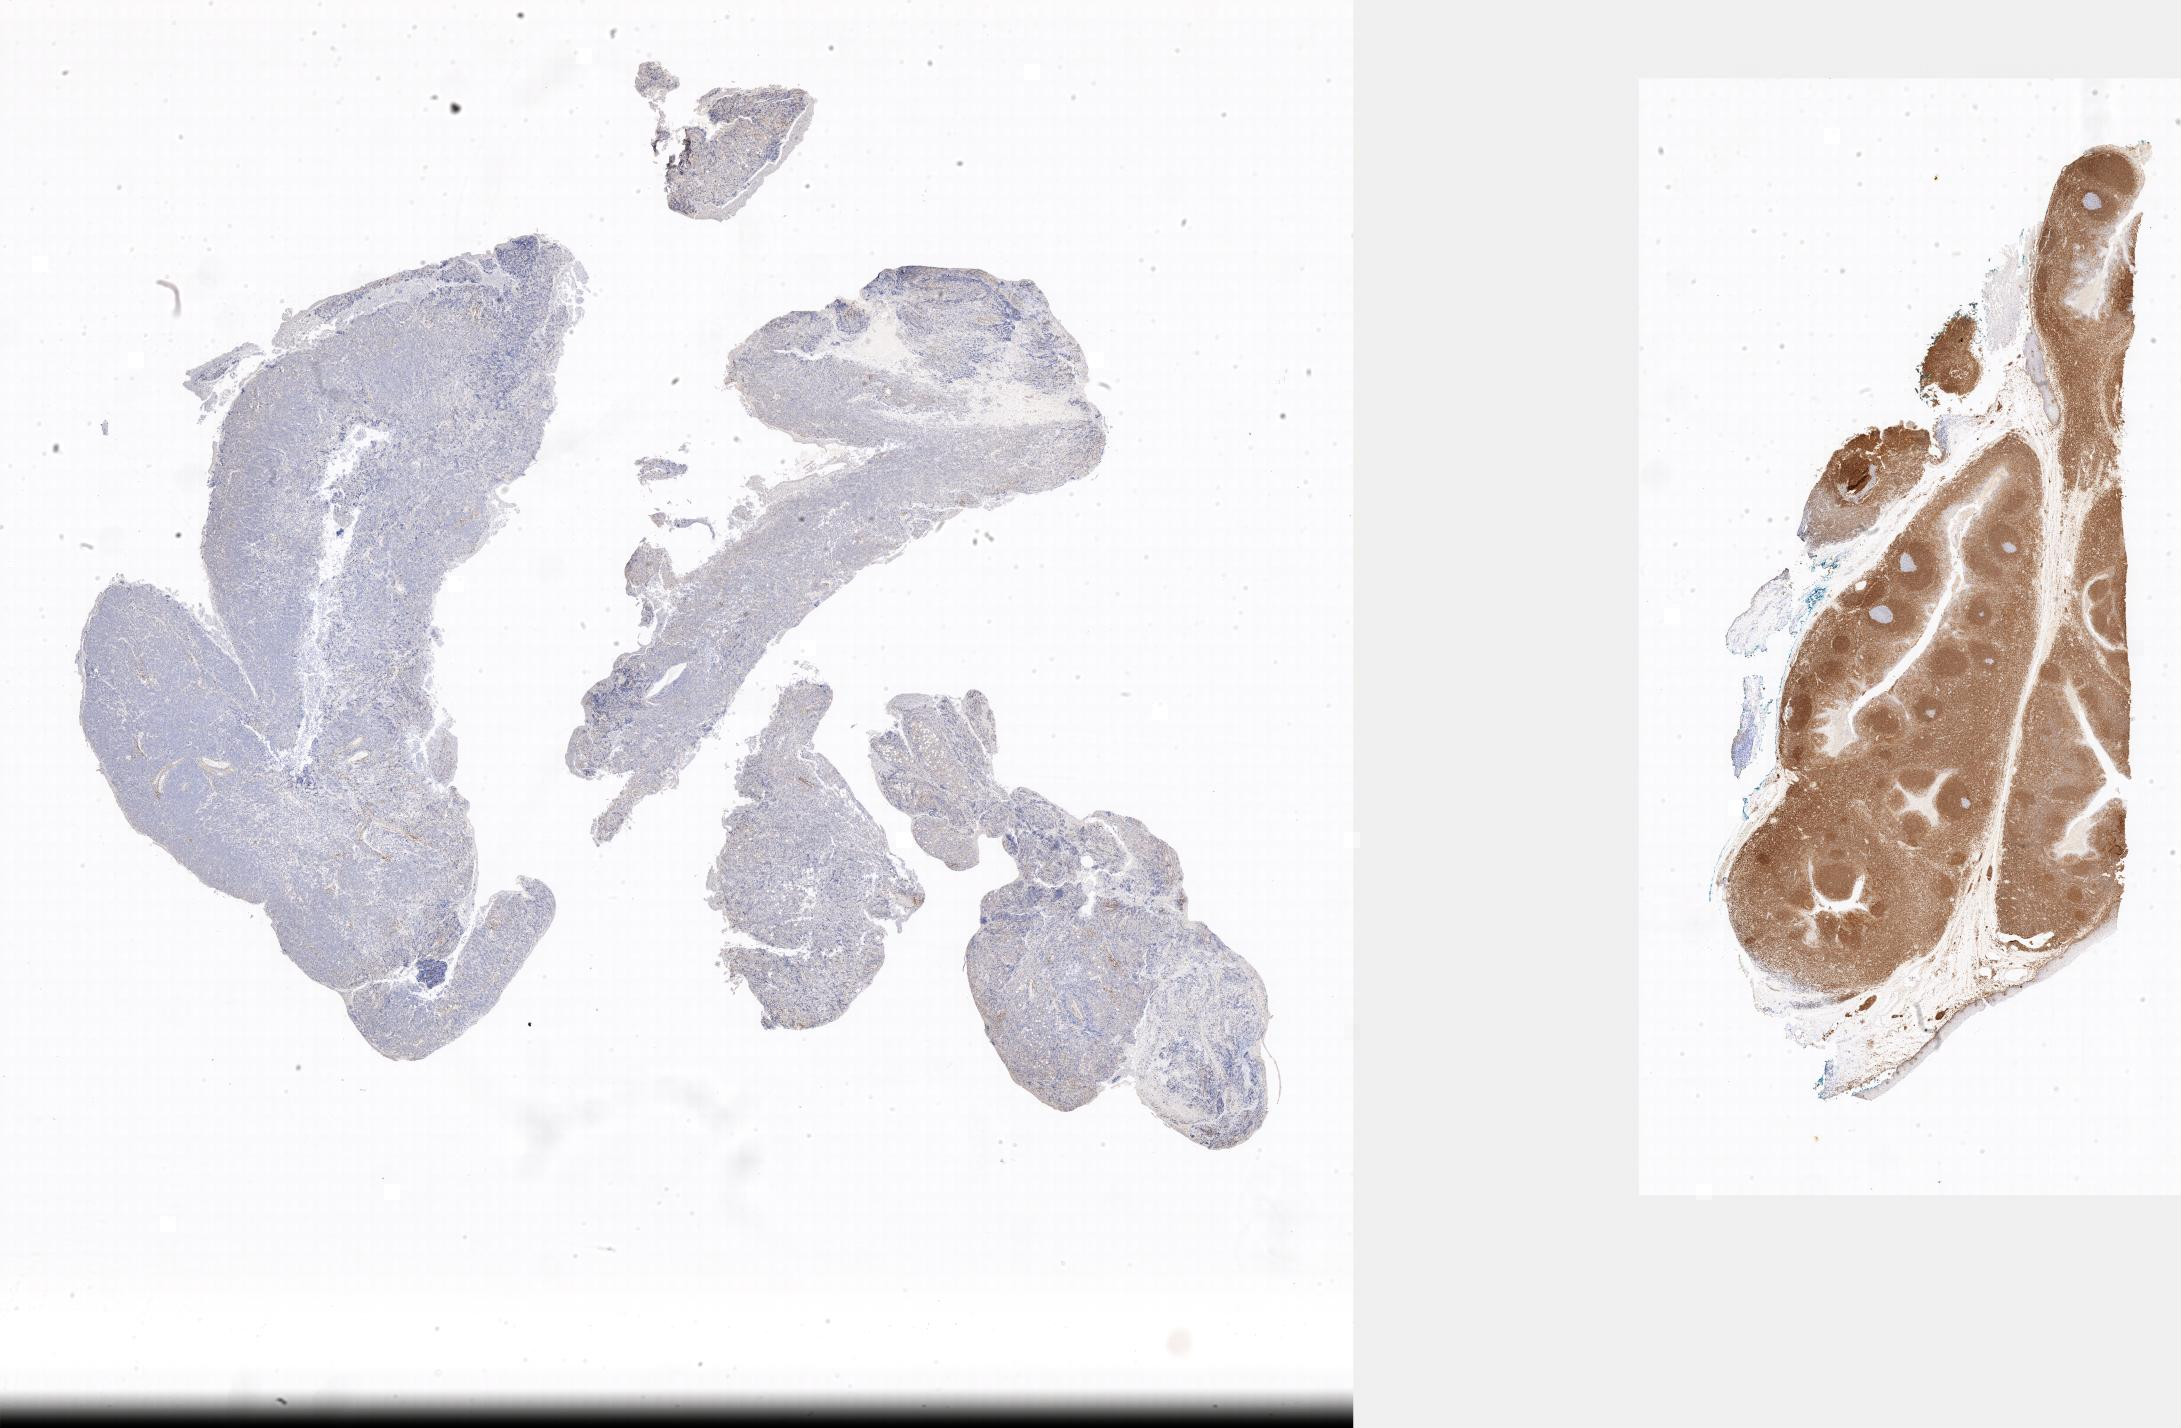
Immunohistochemistry (IHC) whole-slide image stained for BCL2 — low-resolution overview of the scanned area, tumor tissue, anatomic site: abdomen proper. Patient: male, age at initial diagnosis 5 years.
Histologic diagnosis: Burkitt lymphoma, NOS.